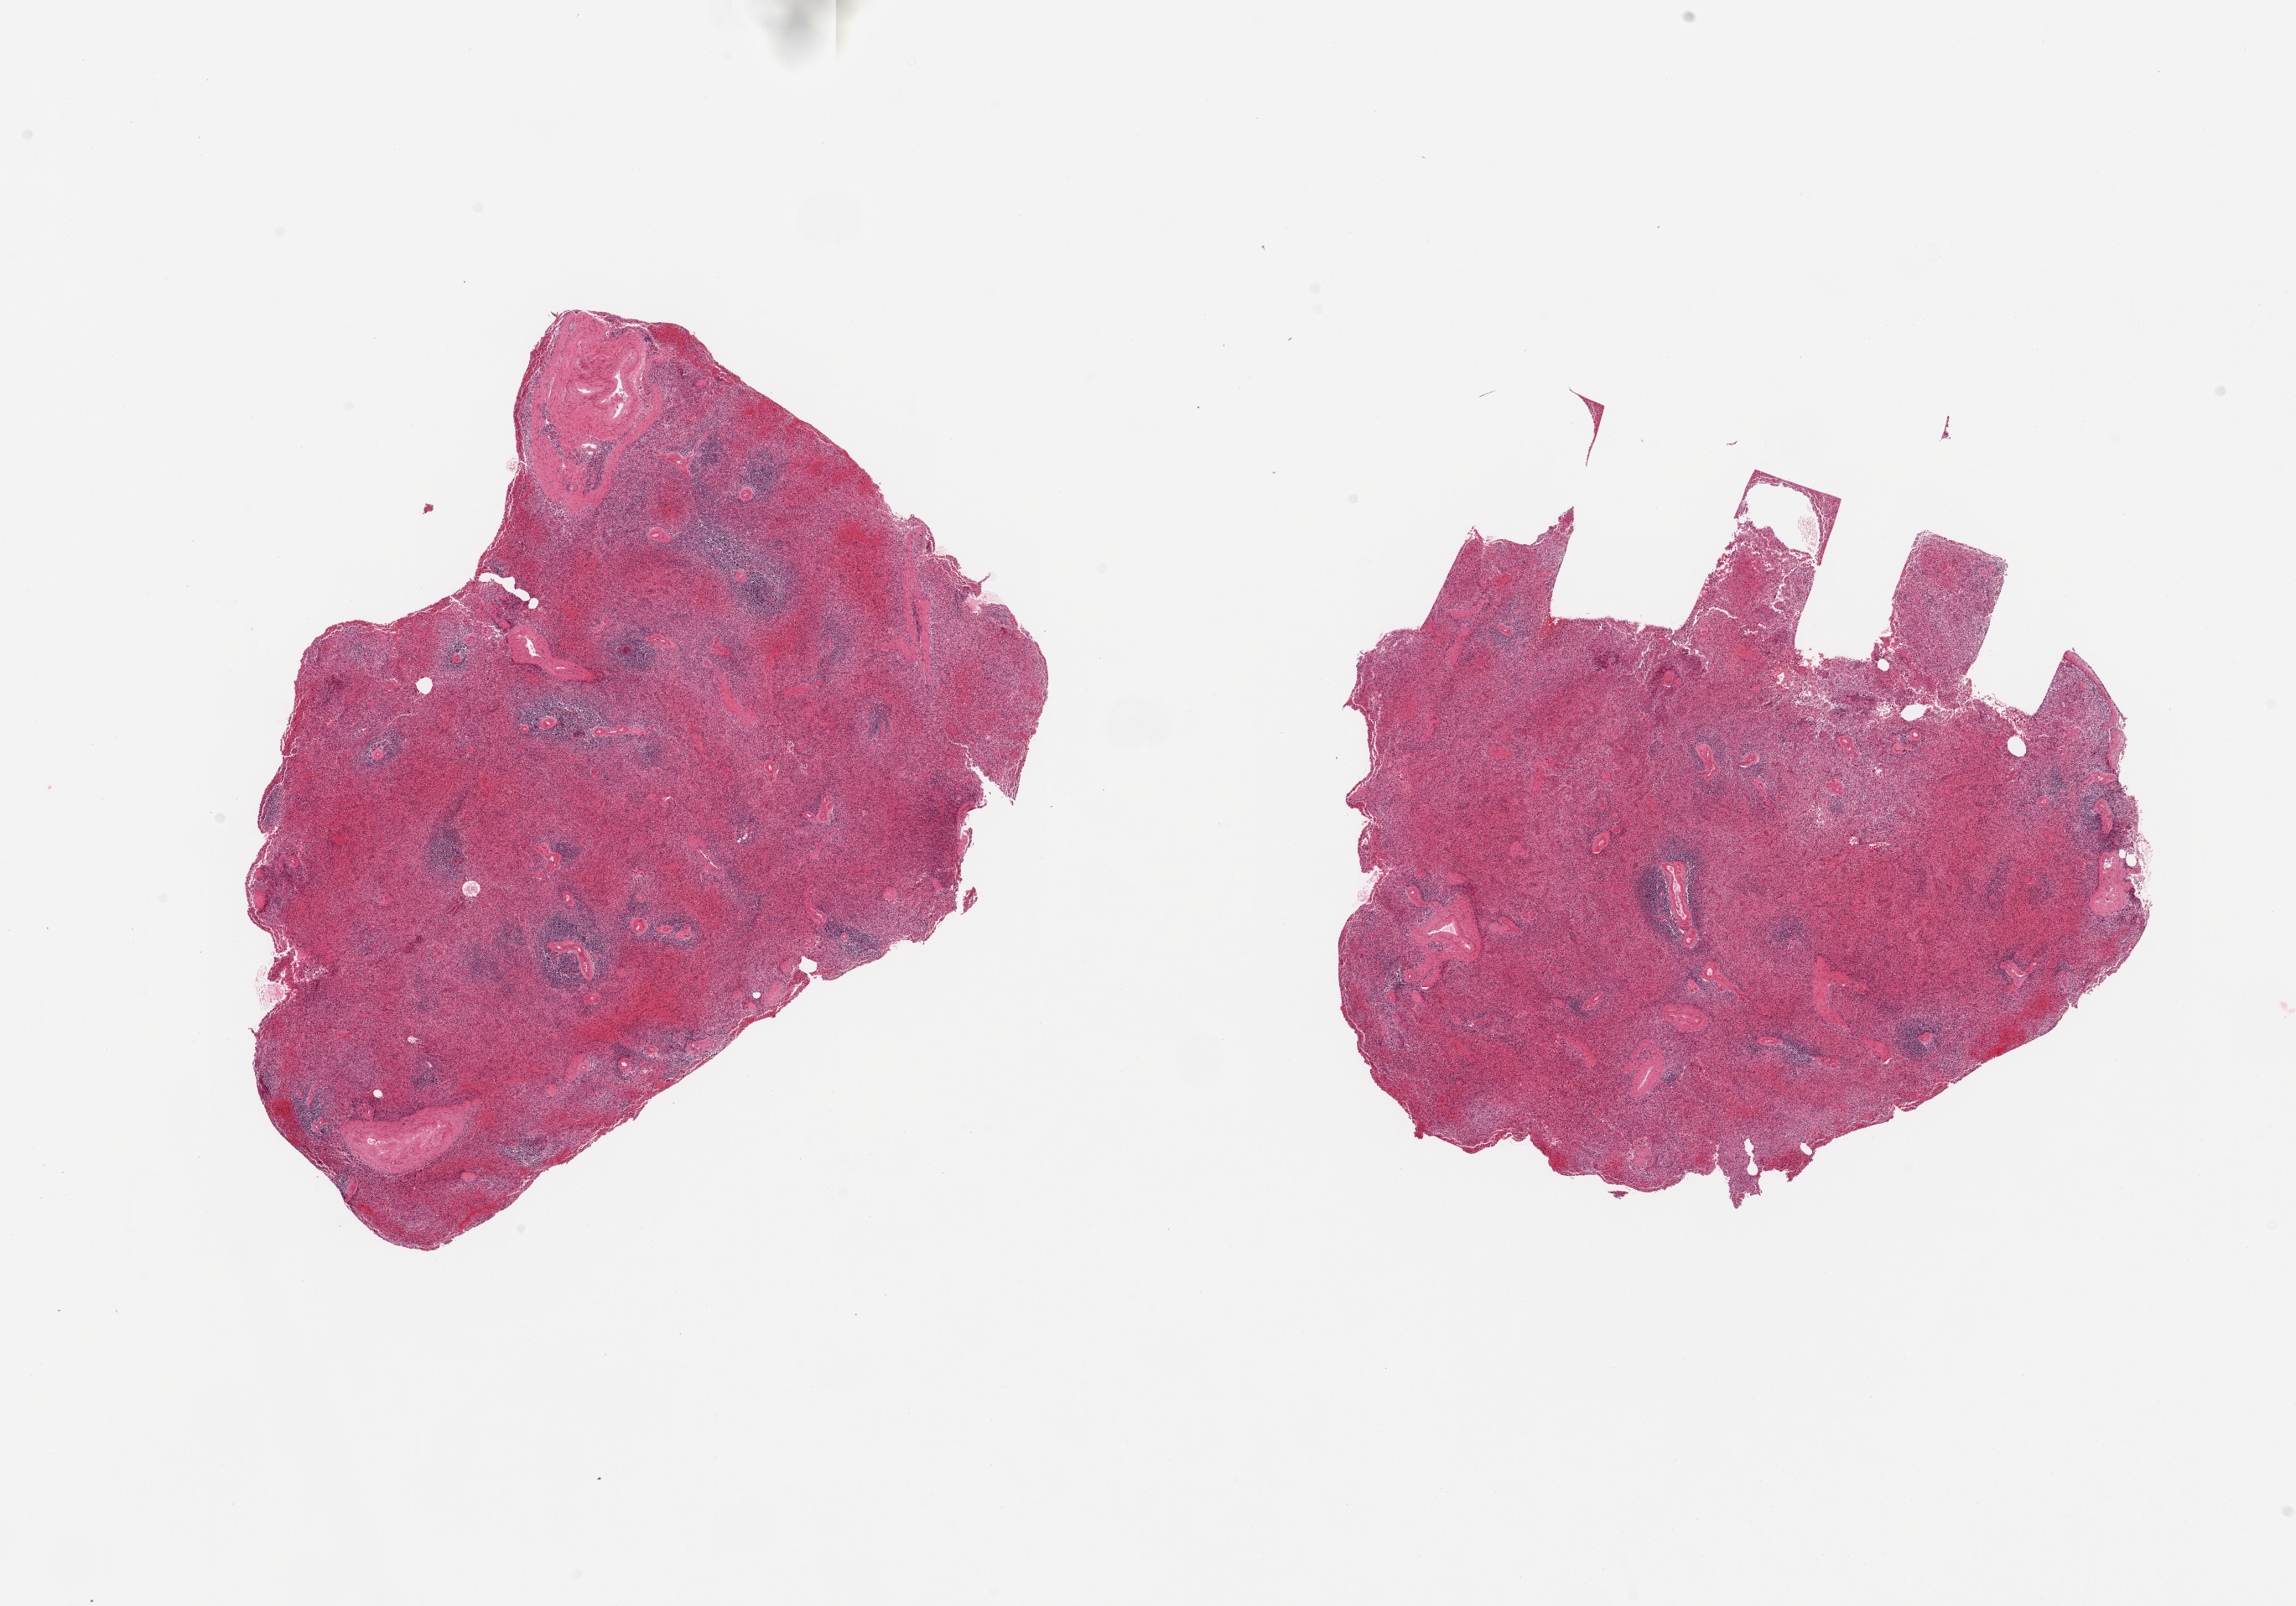
Hematoxylin and eosin (H&E) whole-slide image, a low-resolution overview of the entire scanned area, about 21.7 x 15.1 mm (from a 20x scan), PAXgene-fixed, paraffin-embedded tissue, target tissue: spleen, tissue donor sample. Donor sex: female.
Pathologist's review note for this sample: 2 pieces, marked congestion.